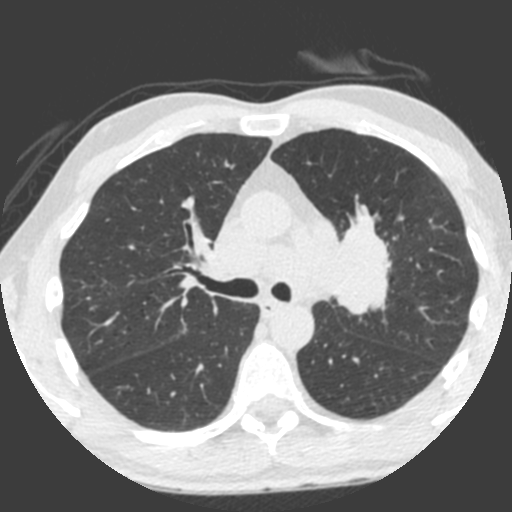
Low-dose screening chest CT, one axial slice; position 141 of 212 along the scan axis; lung window (W 1500 / L -600 HU); 512 × 512 image matrix.
Outlined on this slice (manually delineated by an expert):
- lesion 1 (tumor, upper lobe of left lung): bounding box <332,214,390,315> (left, top, right, bottom; pixels)